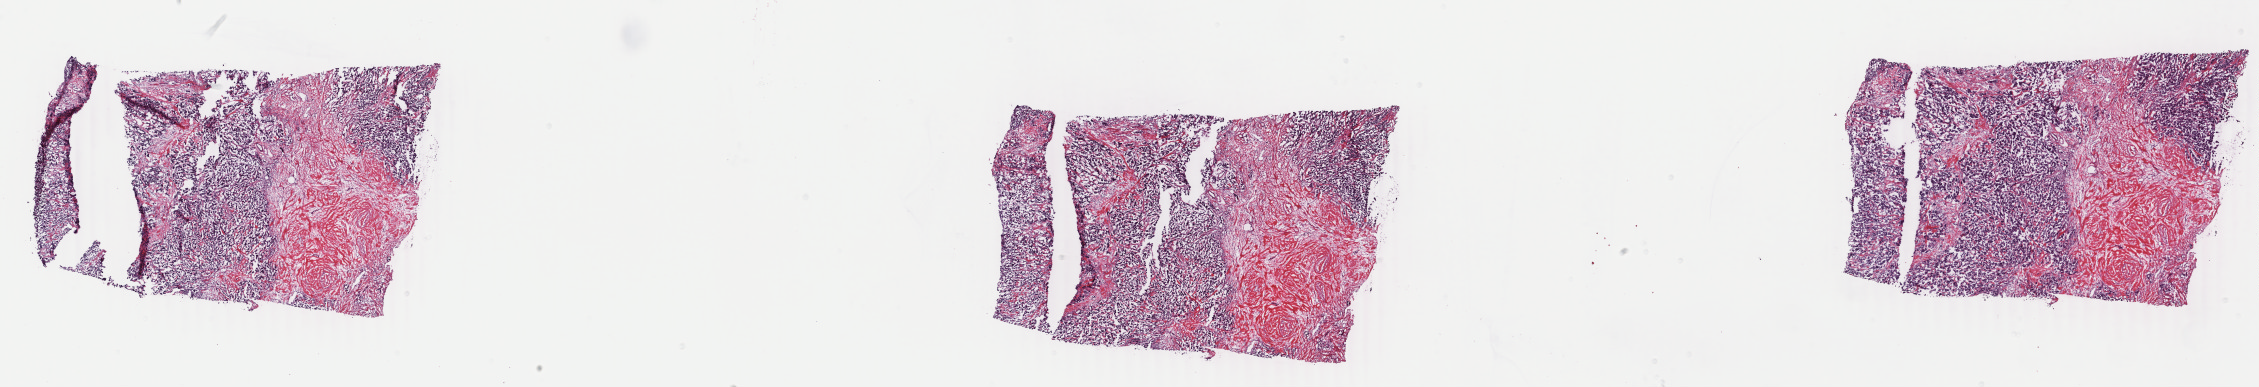
Digitized Hematoxylin and eosin (H&E) stained tissue section (whole slide) — a low-resolution overview of the entire scanned area, about 35.9 x 6.2 mm. Frozen section from the bottom of the tissue portion. Breast, primary tumour sample. Patient: female, age at initial diagnosis 63 years. Slide review estimates, as recorded: tumour cells 65%, tumour nuclei 90%, normal cells 0%, stromal cells 35%, necrosis 0%. Infiltration values recorded for this section: lymphocyte infiltration 0%, monocyte infiltration 0%, neutrophil infiltration 0%.
- diagnosis: Infiltrating duct carcinoma, NOS
- AJCC pathologic stage: IIB
- lymph nodes positive (case pathology): 1 of 7 examined